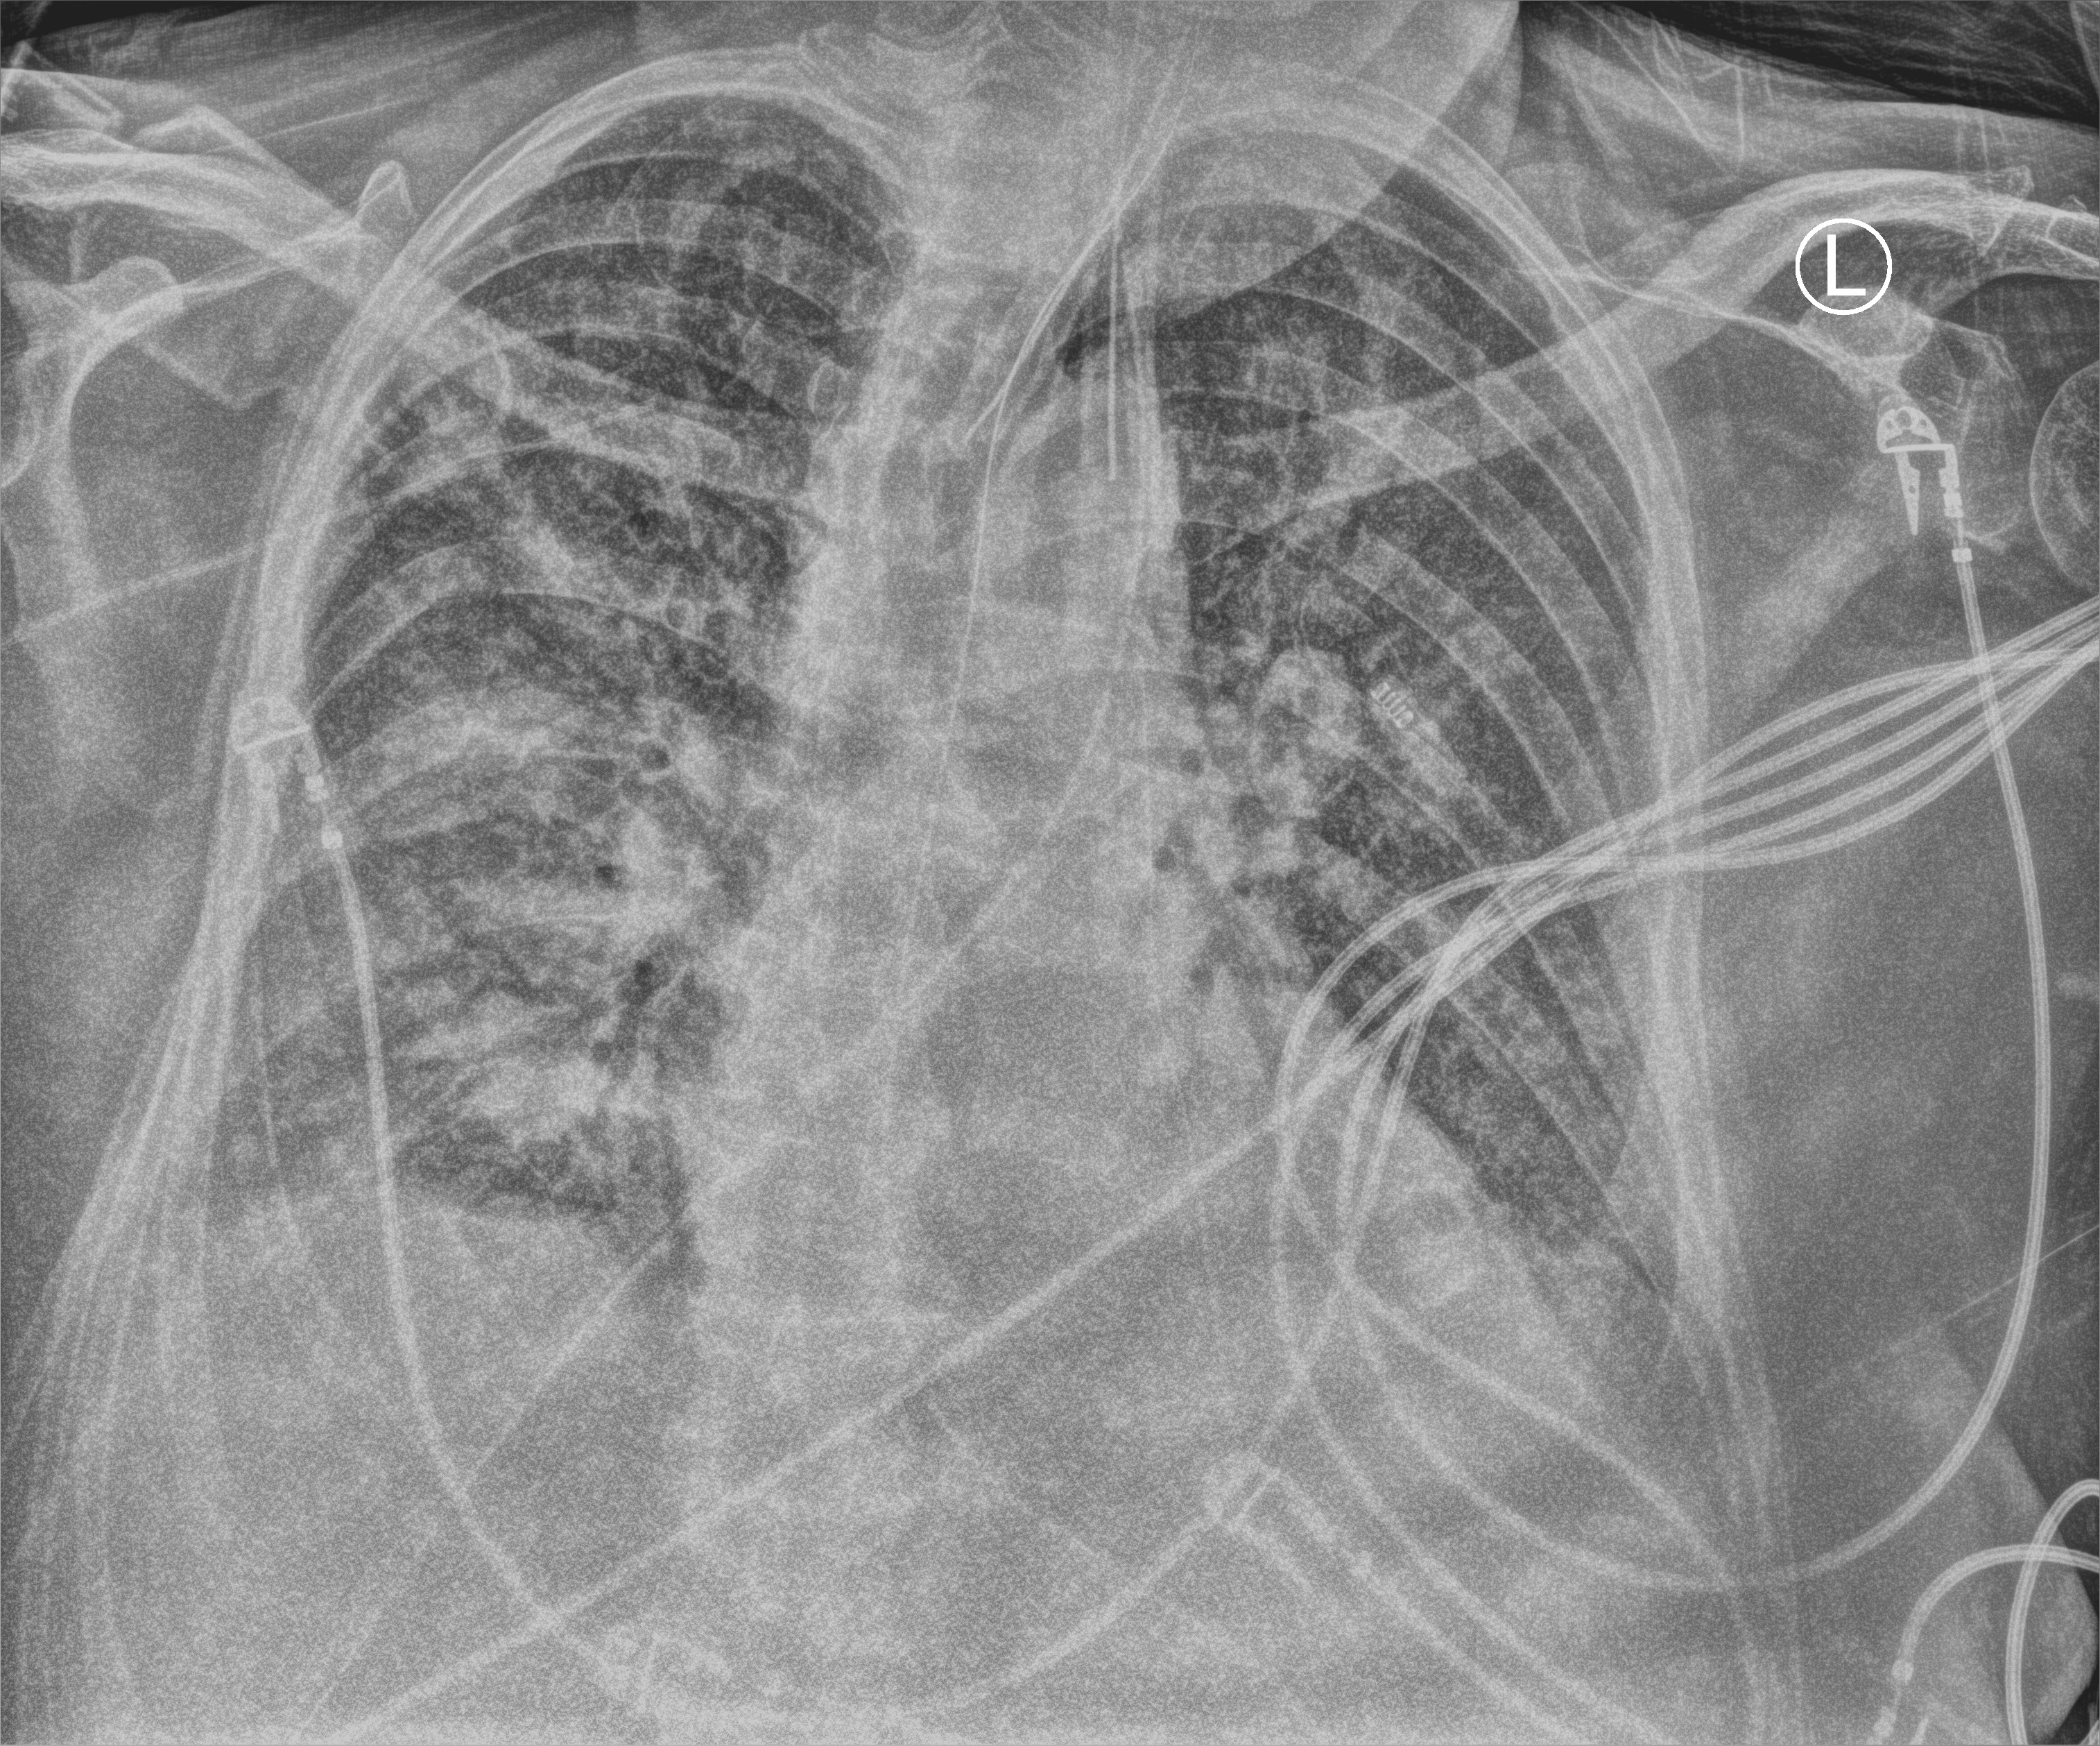
Chest X-ray (portable), anteroposterior (AP) projection. Patient hospitalised with COVID-19; male, aged 60–74 years.
Hospital-stay facts (about this admission, not read from this image; timing relative to this image not recorded): length of hospital stay: 20 days.